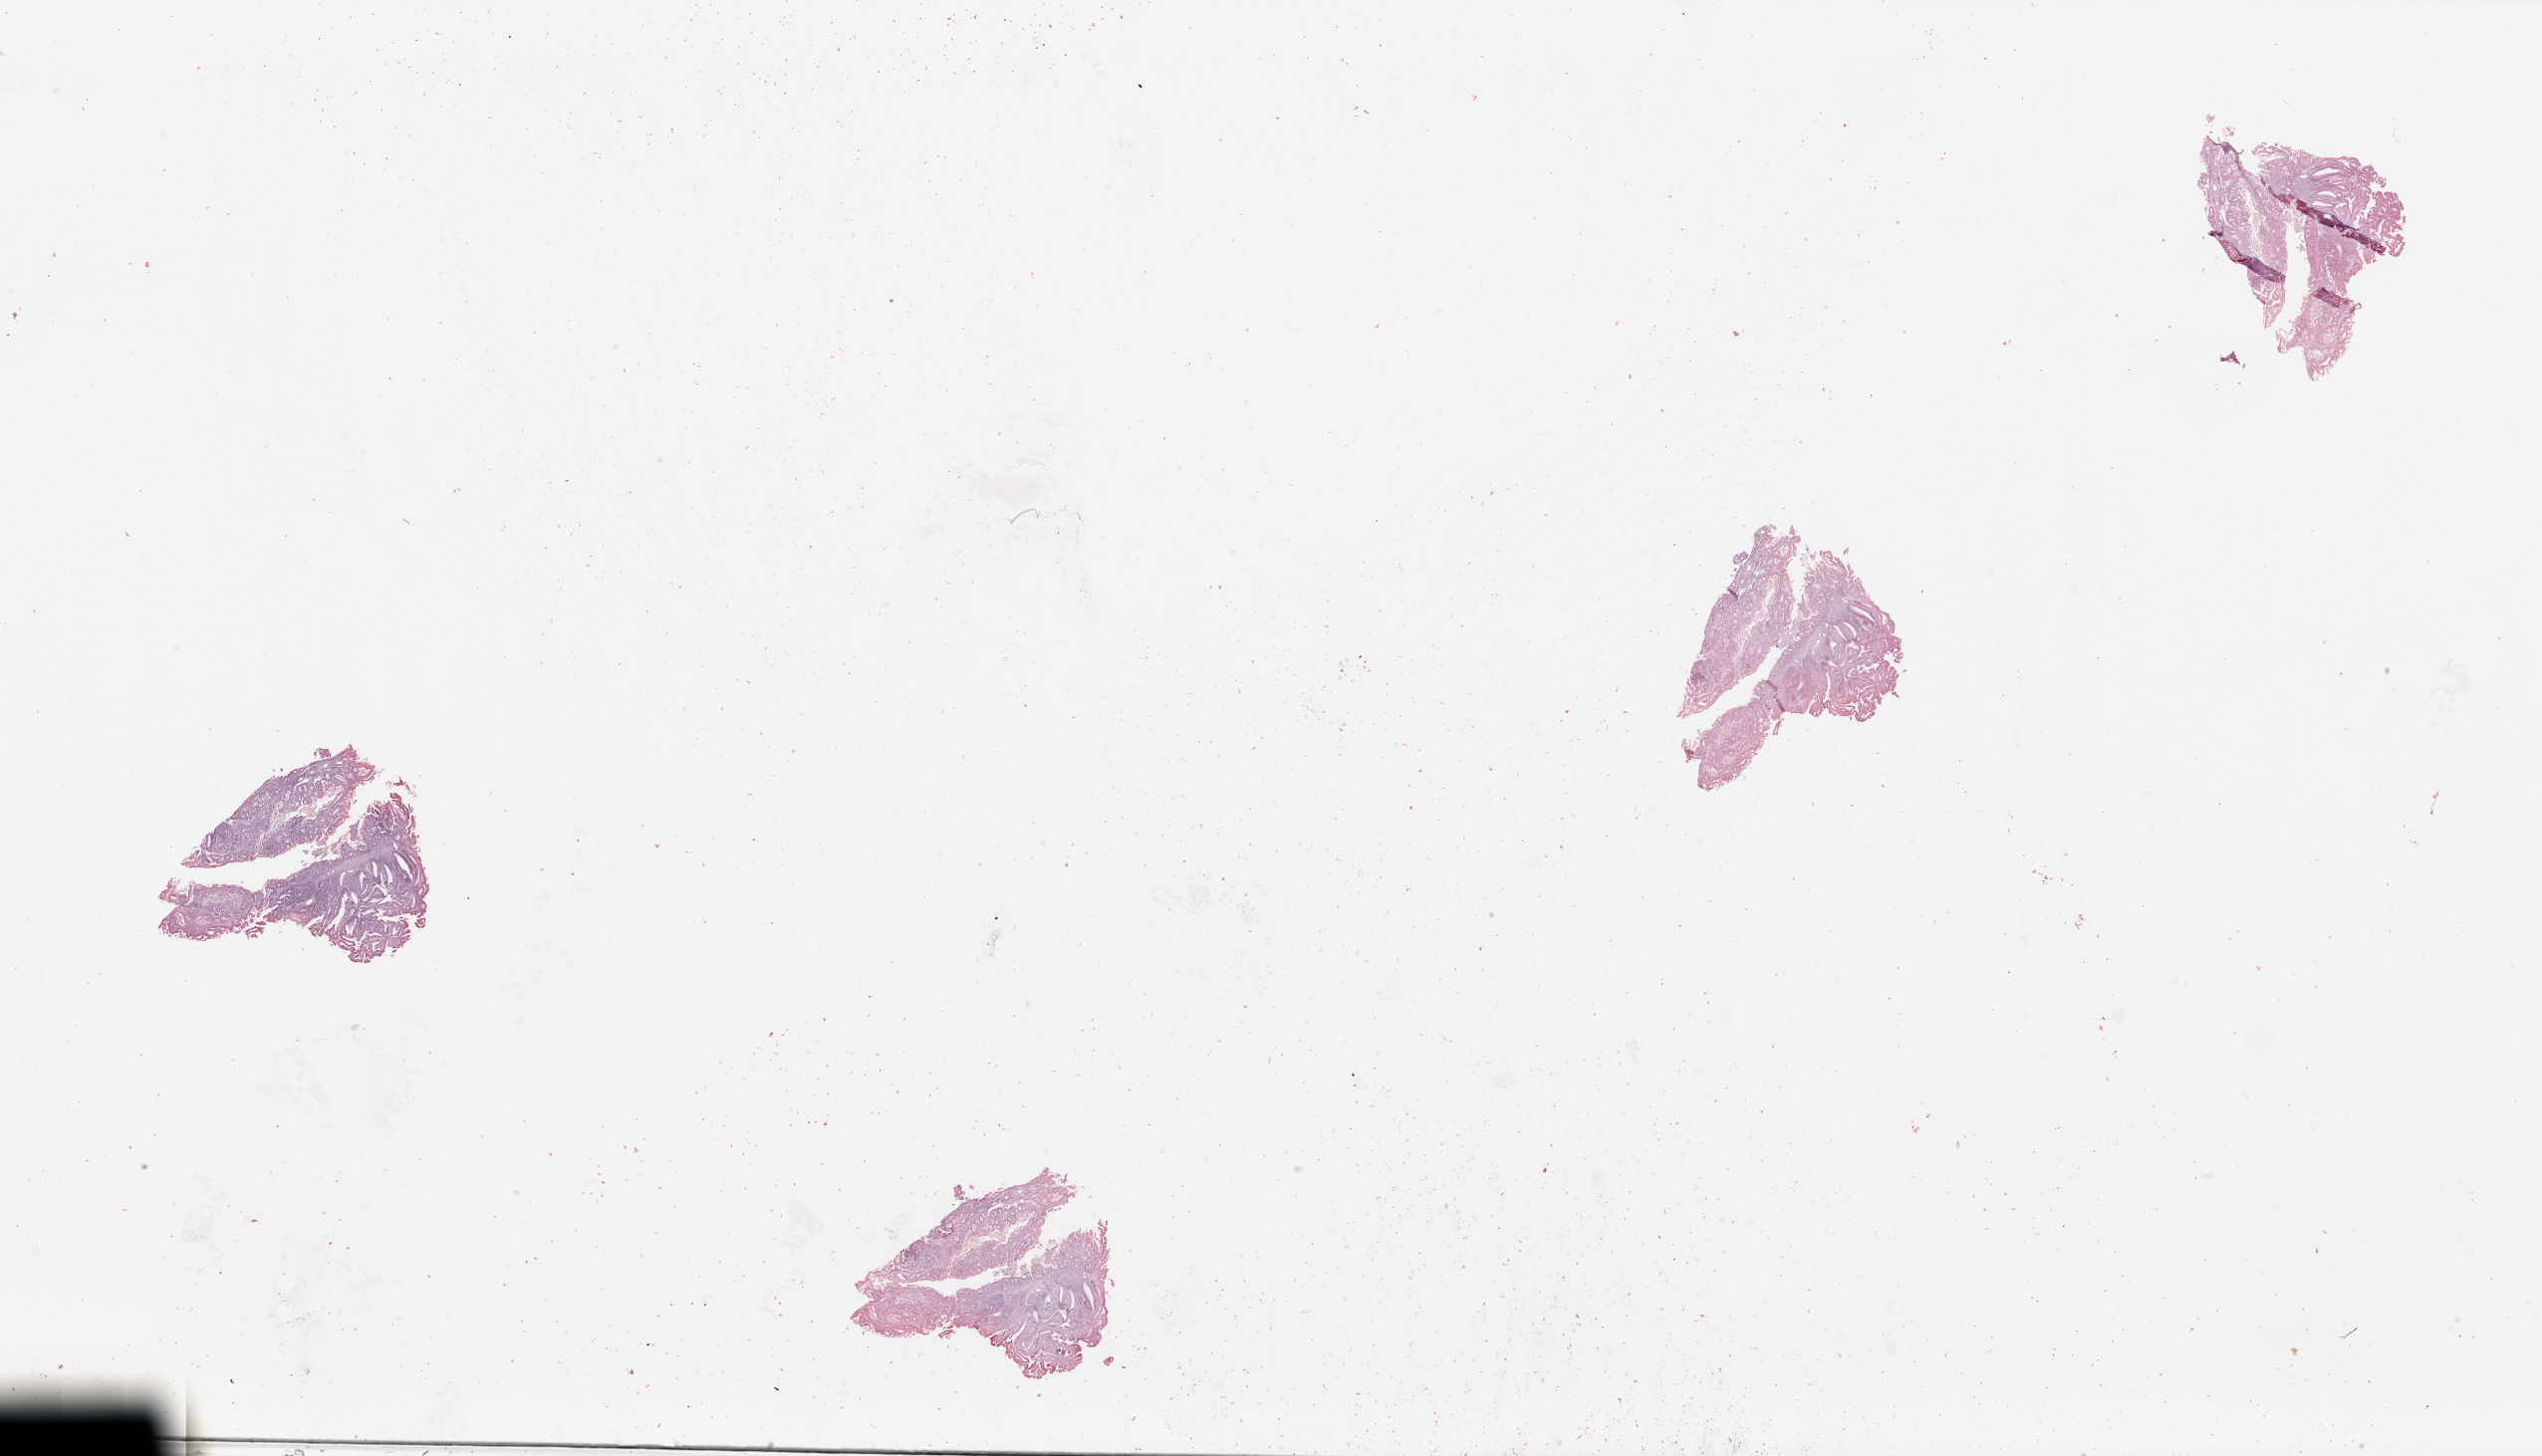
Hematoxylin and eosin (H&E) stained whole-slide image — a low-resolution overview of the entire scanned area, about 40.4 x 23.1 mm (slide scanned at 20x), tumour tissue sample, sampled site: uterus. Female, 60 y/o. Slide review estimates, as recorded: tumour nuclei 80%, necrosis 2%.
Histologic diagnosis: Endometrioid adenocarcinoma, NOS.